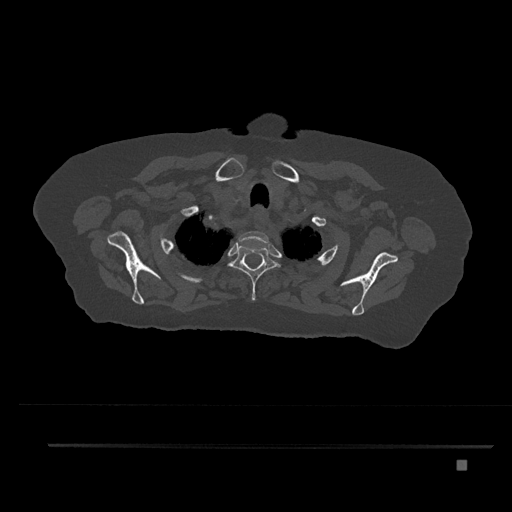
CT including the spine, one axial slice. Reconstruction kernel Br40s/3. 120 kVp. Bone window (W 1800 / L 400 HU). 512 × 512 image matrix. Female patient, age 76 years. Case-level facts recorded for this patient, not image findings: primary cancer: lung.
Structures marked on this image (semi-automatically segmented with operator editing):
- T1 vertebra: bounding box [x1, y1, x2, y2] px = [238, 231, 269, 247]
- T2 vertebra: [228, 242, 281, 300]